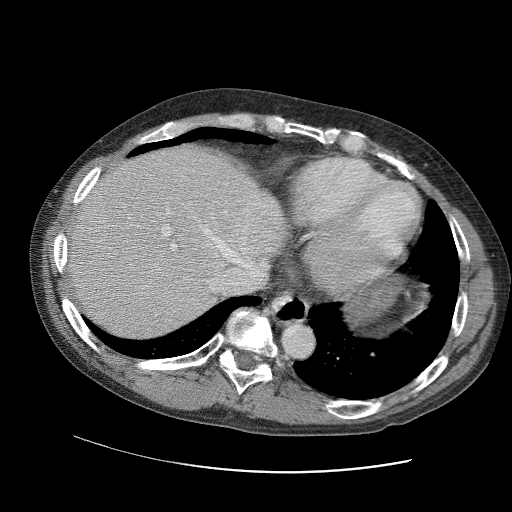
Contrast-enhanced abdominal CT (liver protocol), one axial slice; slice 83 of 109 in the series (ordered by position); reconstruction kernel STANDARD; 120 kVp; soft-tissue window (W 400 / L 40 HU); 2.5 mm slice thickness; 512 × 512 image matrix. From the clinical record (not read from this slice): diagnosis: hepatocellular carcinoma (patient treated with transarterial chemoembolisation; whether this scan precedes or follows treatment is not stated here); TNM stage (as recorded): Stage-IIIC; Child-Pugh class: B; tumour differentiation: well differentiated; tumour nodularity: uninodular.
Structures marked on this image (semi-automatic segmentation, software-assisted and operator-edited):
- abdominal aorta: bounding box [x1, y1, x2, y2] px = [284, 324, 313, 355]
- liver parenchyma outside the tumour (the mass and vessels are separate outlines, so this box may not span the whole liver): [62, 144, 288, 340]
- liver vessels: [100, 195, 276, 316]